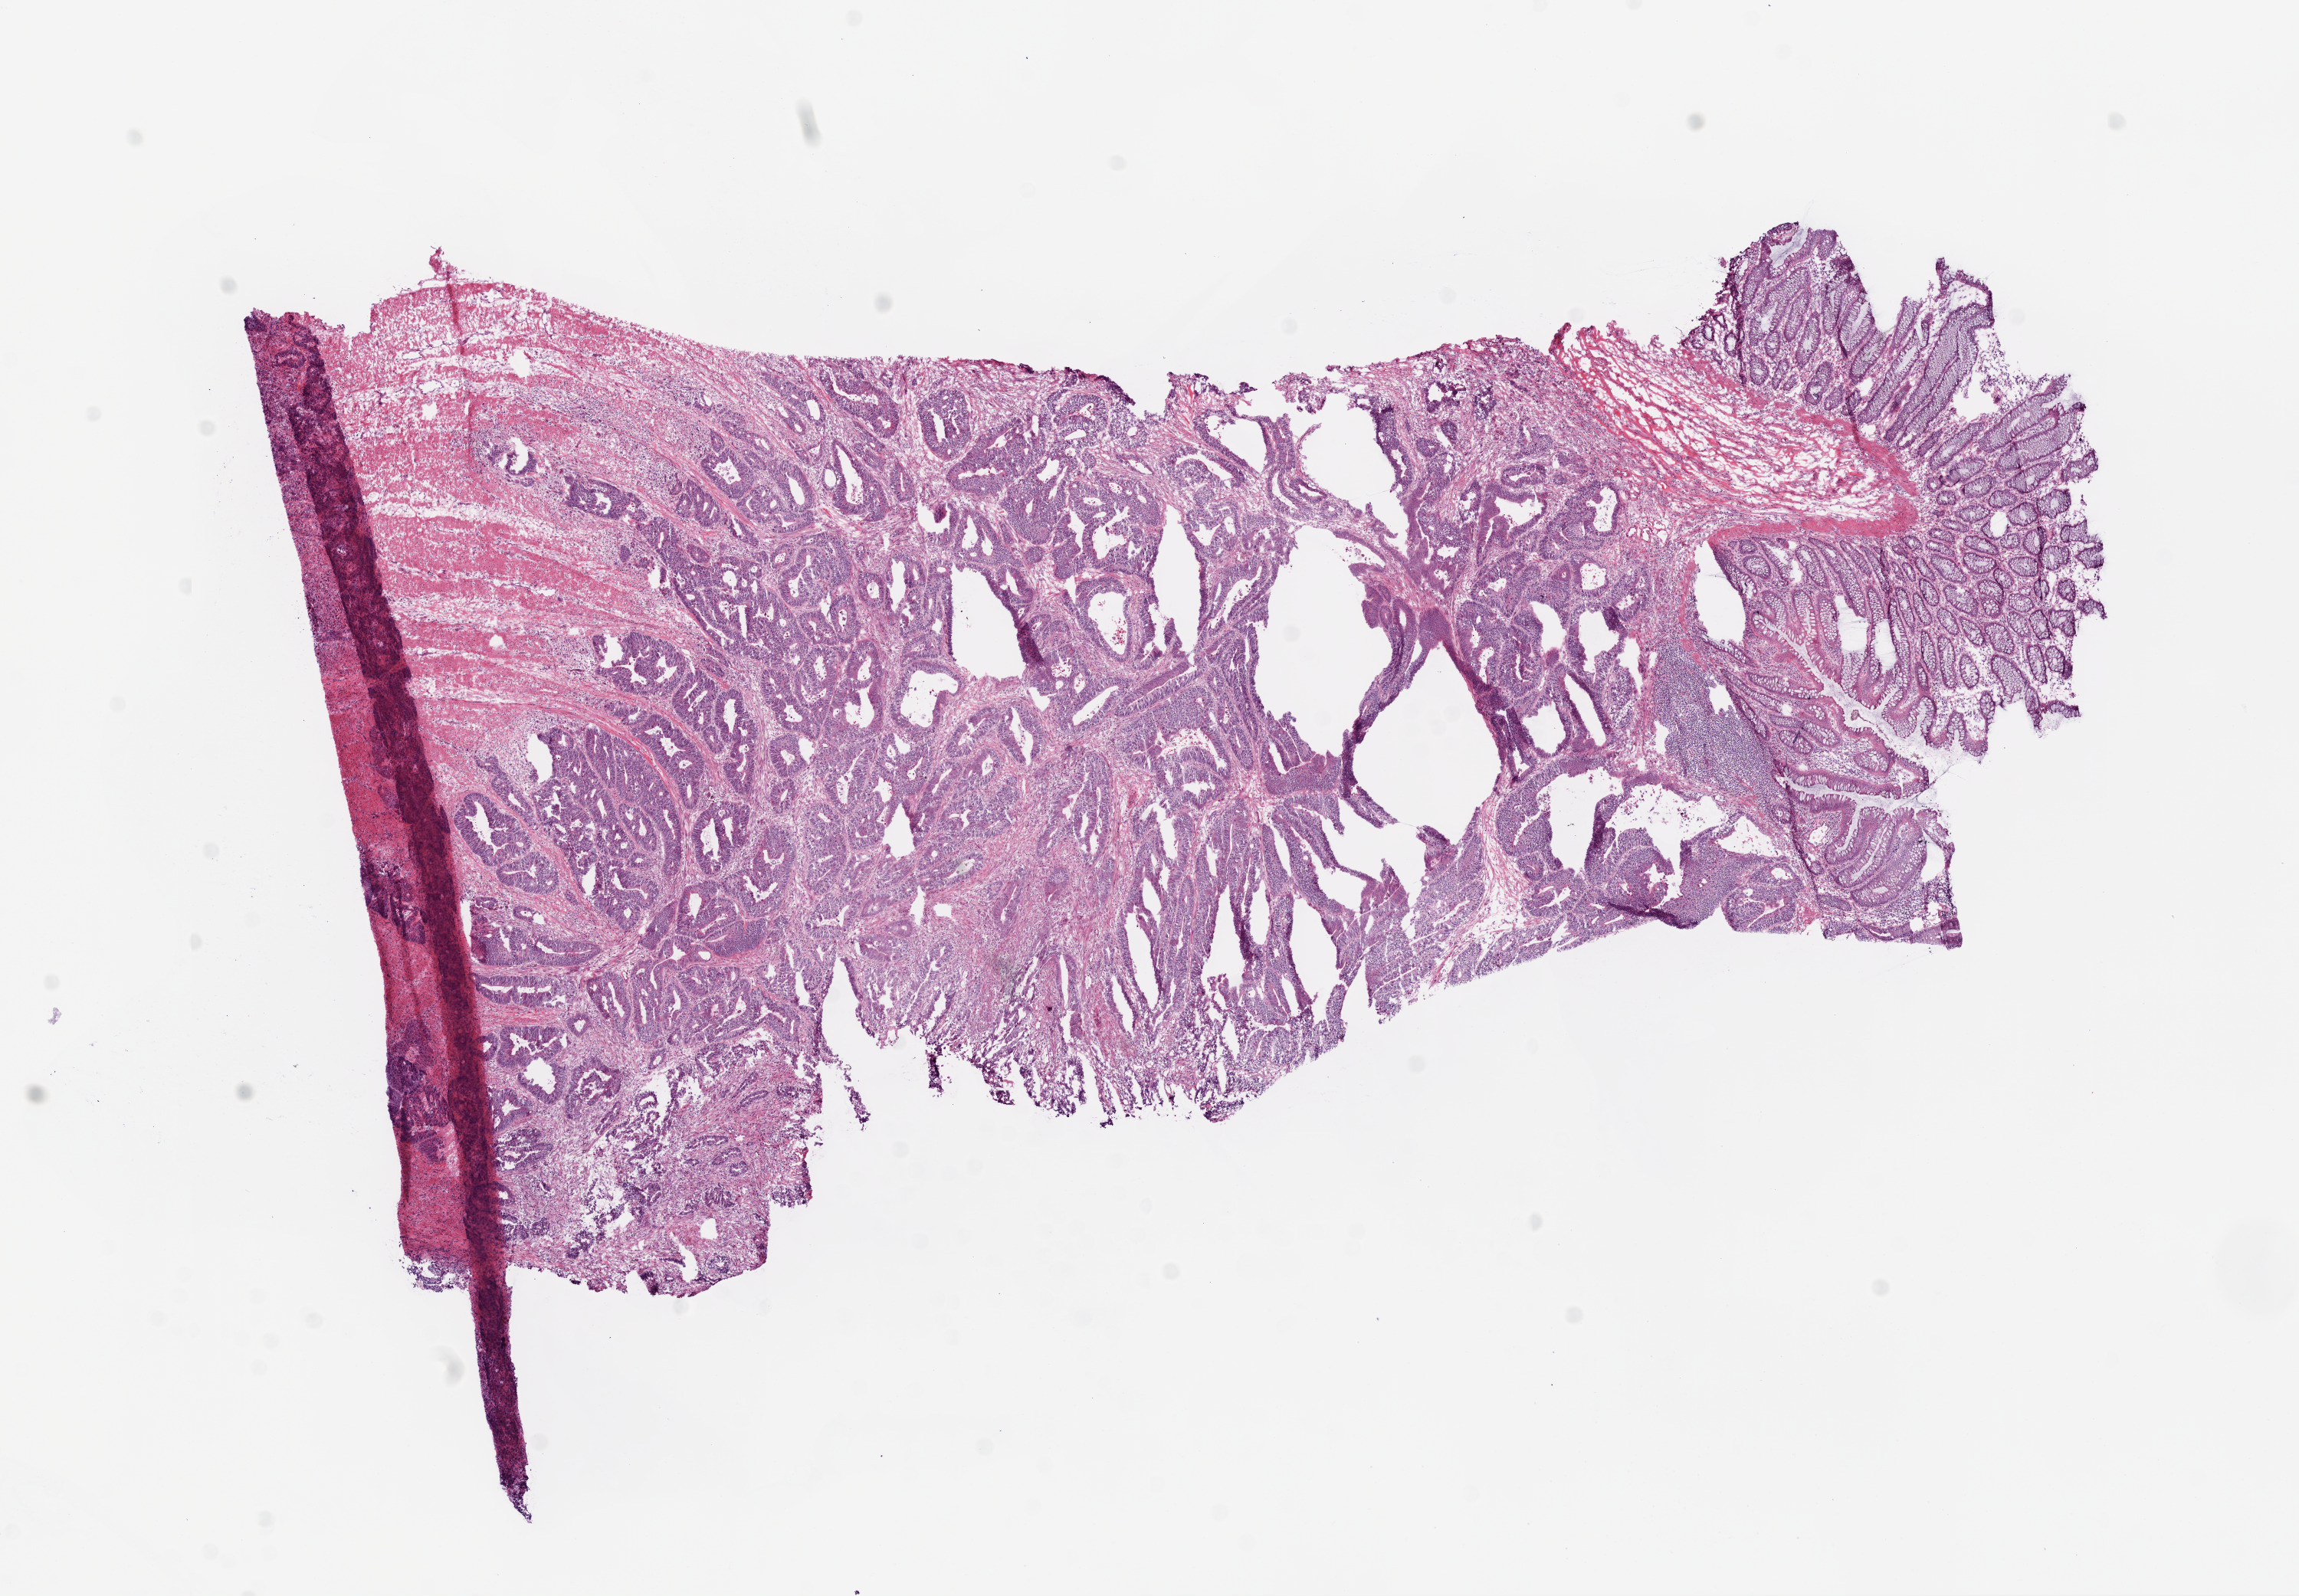
Whole-slide histology image, H&E-stained — whole scanned area (about 12.0 x 8.4 mm) shown as a low-resolution overview, frozen section, sample: primary tumour, colon. Male patient; age at initial diagnosis 87 years. Slide review estimates, as recorded: tumour cells 80%, tumour nuclei 90%, normal cells 0%, stromal cells 20%, necrosis 0%.
- pathologic diagnosis: Adenocarcinoma, NOS (sigmoid colon)
- lymph nodes positive (case pathology): 0 of 22 examined
- AJCC pathologic stage: II (5th edition)